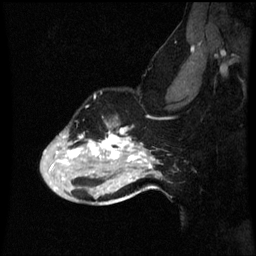
Breast MRI (dynamic contrast-enhanced), one sagittal slice; position 44 of 60 along the scan axis; dynamic contrast-enhanced series, image 2 of 3 at this slice position (ordered by acquisition); 1.5 T; TE 4.2 ms, TR 8.9 ms; 2 mm slice thickness; 256 × 256 image matrix, field of view 200 × 200 mm. Patient: female, 49 years. Case-level facts recorded for this patient, not image findings: setting: breast cancer imaged before/during neoadjuvant chemotherapy; receptor status: HR-positive, HER2-negative.
Structures marked on this image (semi-automatically segmented with operator editing):
- analysis volume of interest (the breast-tissue region the enhancement analysis was run in; not a lesion): bounding box <42,118,159,199> (left, top, right, bottom; pixels)
- tumour enhancement mask (voxels above the 70 % enhancement threshold inside the analysis volume of interest): <56,130,155,169>